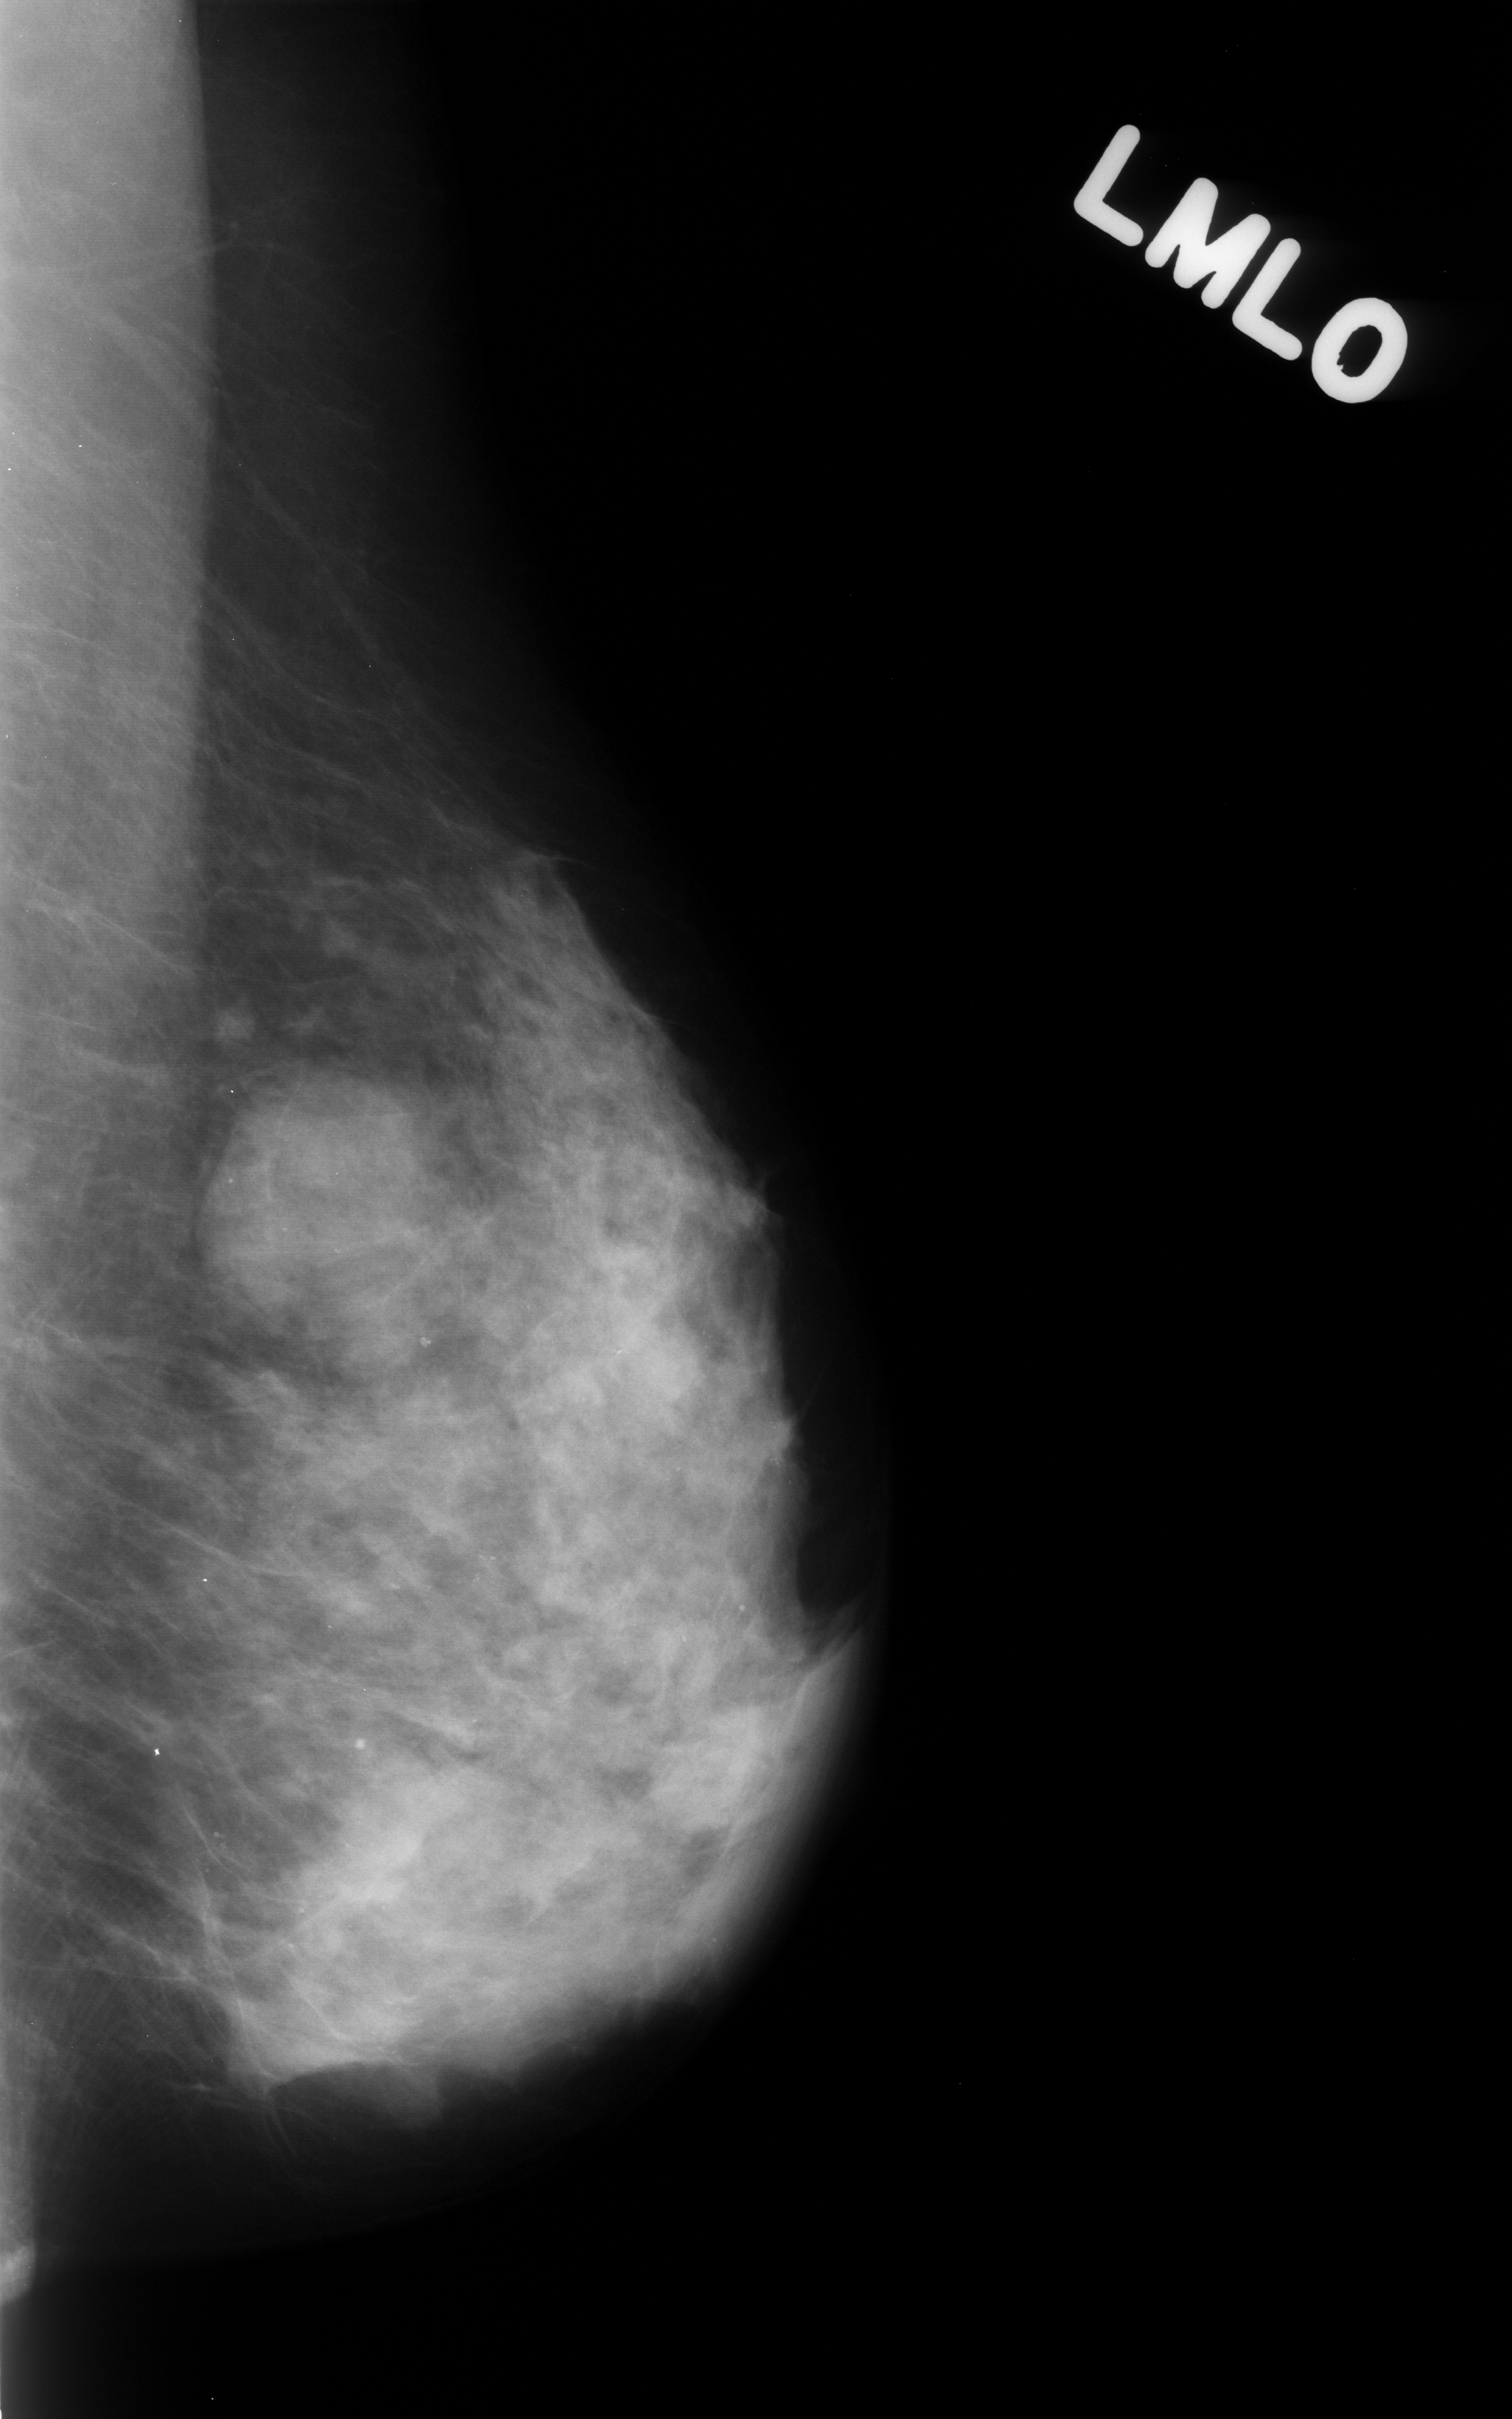
Scanned film-screen mammogram; left breast; mediolateral oblique (MLO) view; BI-RADS breast density category 3 (scale 1–4).
- Abnormality record for this image: calcifications, morphology pleomorphic, distribution diffusely scattered; BI-RADS assessment category 3; pathology result (as recorded, not read from the image): benign.